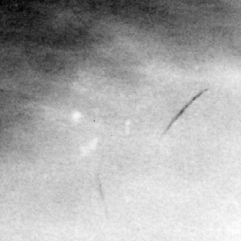
Cropped region of a digitized screen-film mammogram centred on a radiologist-marked abnormality; right breast; CC view.
Marked abnormality: calcifications, morphology pleomorphic, distribution clustered; BI-RADS assessment category 4; subtlety rating 4 on a 1 (subtle) to 5 (obvious) scale; pathology (as recorded): malignant.